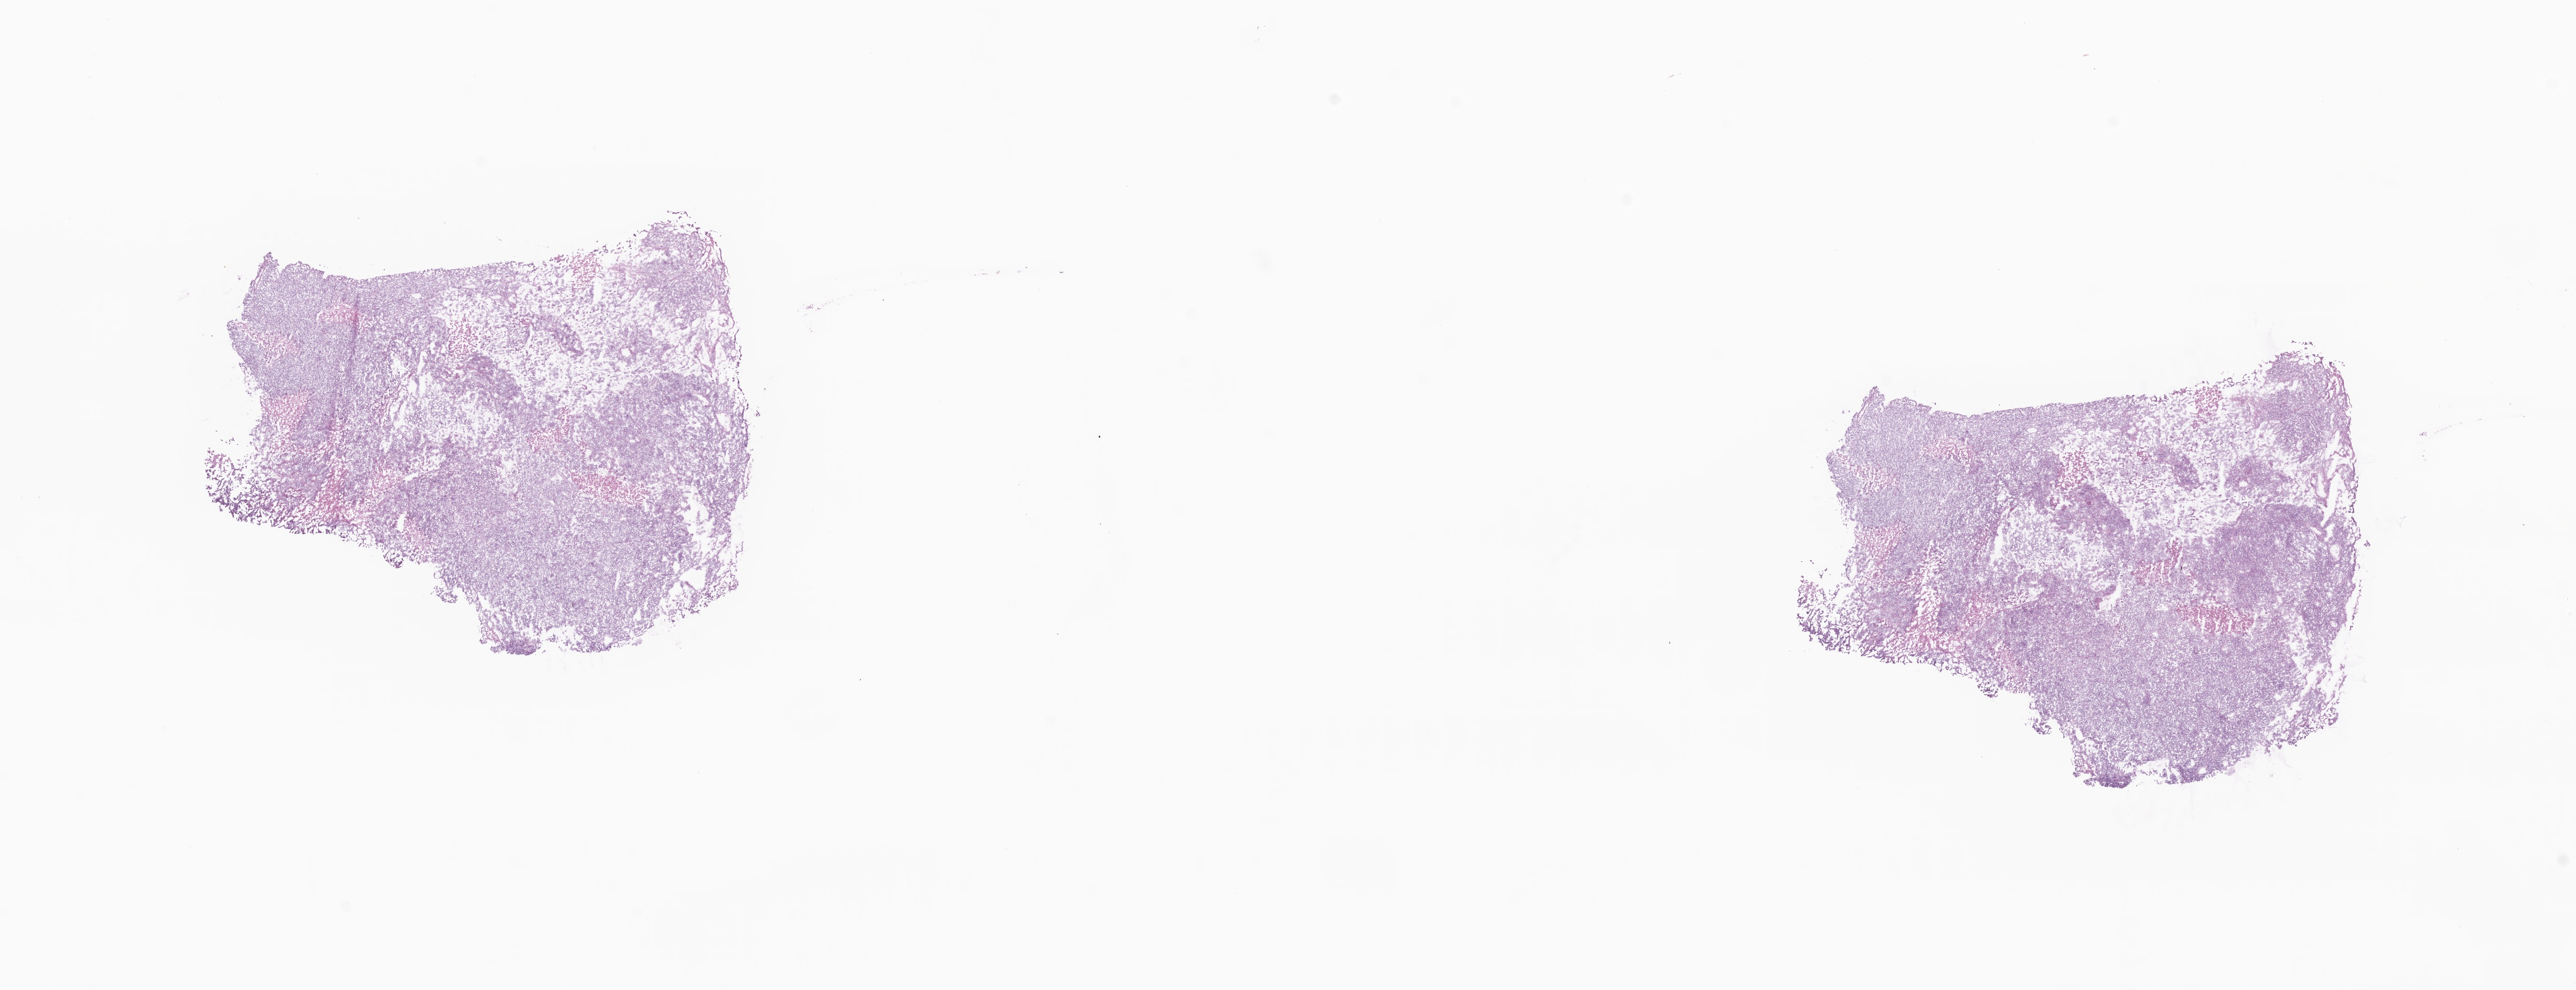
Digitized haematoxylin and eosin-stained section — whole scanned area (about 23.2 x 8.9 mm) shown as a low-resolution overview. Frozen section (tissue freezing medium). Specimen: primary tumor. Anatomic site: body of uterus. Female patient. Tumor grade: G3 (poorly differentiated). Slide review estimates, as recorded: tumor cells 80%, tumor nuclei 80%, stromal cells 10%, necrosis 10%, normal cells 0%. Infiltration values recorded for this section: lymphocyte infiltration 3%, monocyte infiltration 1%, neutrophil infiltration 3%.
• histologic diagnosis: Carcinoma, undifferentiated, NOS
• AJCC pathologic stage: Stage IA